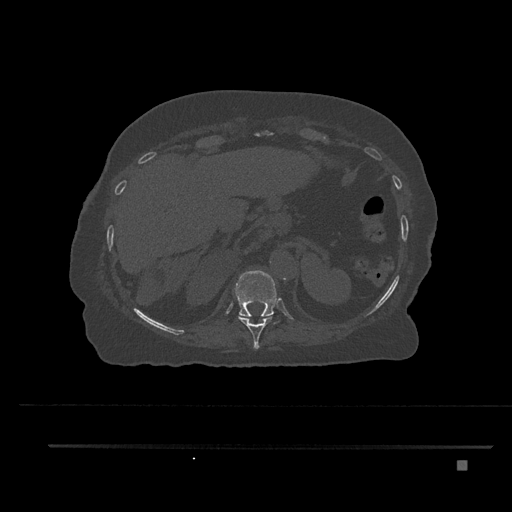
CT including the spine, one axial slice; slice 332 of 797 in the series (ordered by position); reconstruction kernel Br40s/3; 120 kVp; bone window (W 1800 / L 400 HU); 512 × 512 image matrix, field of view 437 × 437 mm. Patient: female, 76 years. Case-level facts recorded for this patient, not image findings: primary cancer: lung.
Structures marked on this image (semi-automatic segmentation, software-assisted and operator-edited):
- T10 vertebra: bounding box [x1, y1, x2, y2] px = [238, 315, 272, 349]
- T11 vertebra: [234, 270, 278, 324]